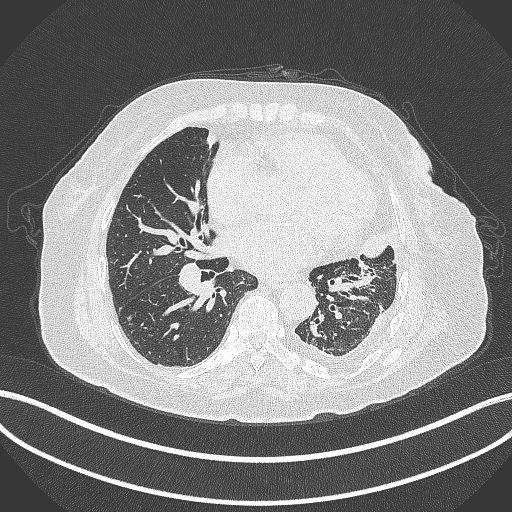
Chest CT, one axial slice; slice 165 of 399 in the series (ordered by position); reconstruction kernel B70f; 120 kVp; lung window (W 1500 / L -600 HU); 512 × 512 image matrix, field of view 400 × 400 mm. Patient: female, 75 years. Case-level facts recorded for this patient, not image findings: clinical TNM (as recorded): T3 N3 M1.
Outlined on this slice (rectangle marked by the reading radiologist):
- lung tumour (recorded histology: adenocarcinoma): bounding box (x1, y1, x2, y2) in pixels: (361, 226, 398, 262)